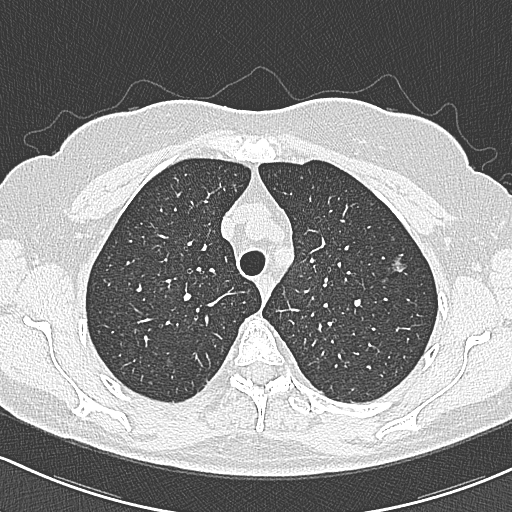
Axial slice from a low-dose chest CT screening exam. Baseline annual screen. Lung window (W 1500 / L -600 HU). 1 mm slice thickness. Female participant, aged 65 years at enrolment. Current smoker at enrolment.
Lesion marked by an expert reader, bounding box (x1, y1, x2, y2) in pixels: (379, 246, 417, 285). The screening reader recorded 3 non-calcified nodules or masses ≥4 mm on this exam (left upper lobe, left upper lobe, right upper lobe); which of them this box marks is not recorded. Lung cancer was diagnosed 390 days after this screen (after the second annual screen): bronchiolo-alveolar carcinoma, non-mucinous, left upper lobe, stage IA (AJCC 6th edition), 10 mm at pathology.